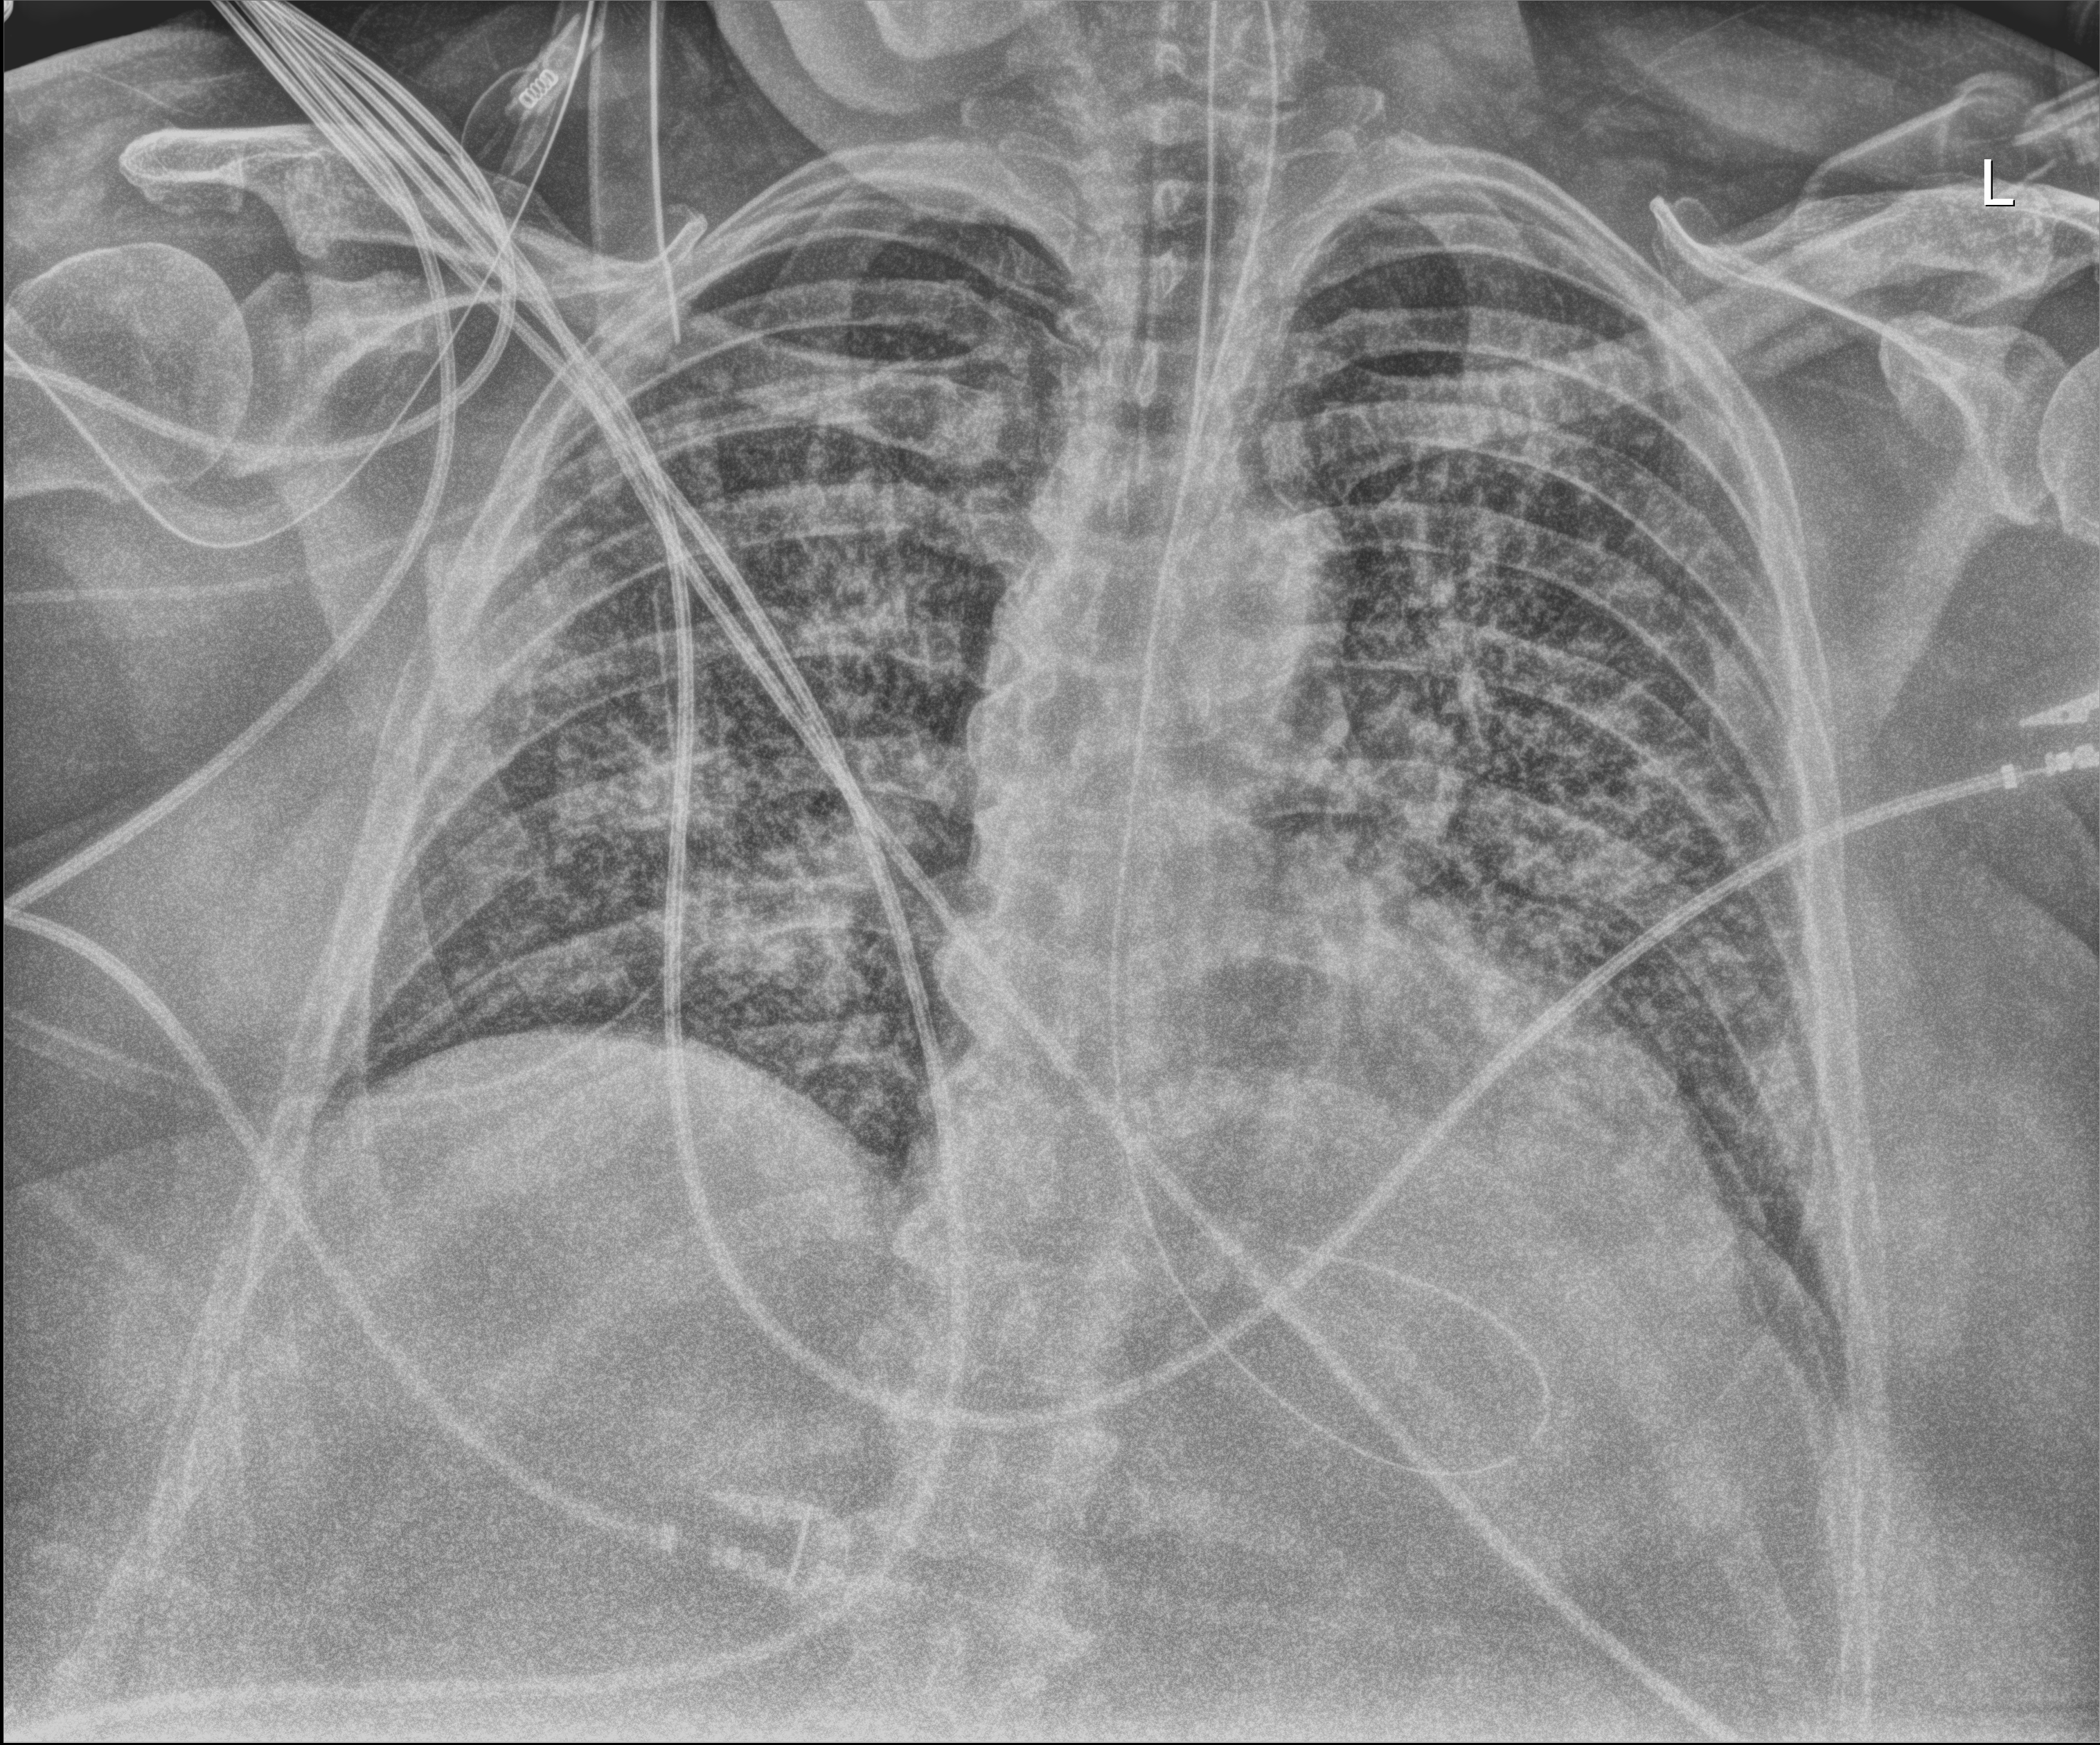
Chest radiograph (digital radiography), anteroposterior (AP) projection. Adult patient hospitalised with COVID-19, age 18–59 years.
Admission-level facts for this patient (not findings on this image; timing relative to this image not recorded):
- admitted to intensive care during this hospital stay: yes
- mechanically ventilated during this hospital stay: yes